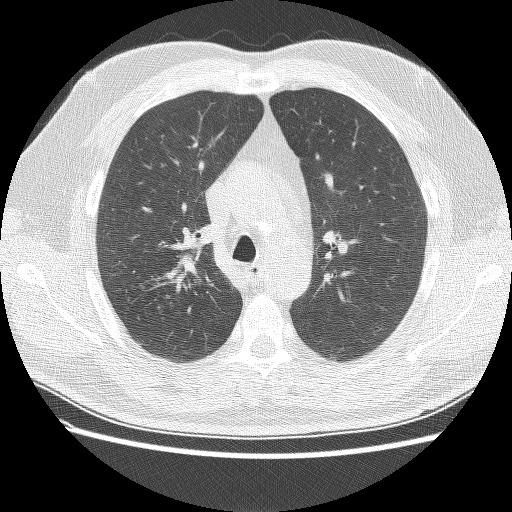
Axial slice from a low-dose chest CT screening exam; baseline screening round; lung window (W 1500 / L -600 HU); 2.5 mm slice thickness; 512 × 512 image matrix, field of view 360 × 360 mm. Male participant, aged 57 years at enrolment. Current smoker at enrolment.
Lesion marked by an expert reader, box from (x=155, y=241) to (x=213, y=293) px. No non-calcified nodule or mass ≥4 mm was recorded by the screening reader at this exam.